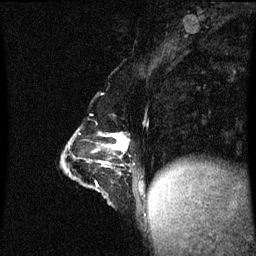
Breast MRI (dynamic contrast-enhanced), one sagittal slice. Position 22 of 60 along the scan axis. Dynamic contrast-enhanced series, image 2 of 3 at this slice position (ordered by acquisition). 1.5 T. TE 4.2 ms, TR 8.9 ms. 2 mm slice thickness. 256 × 256 image matrix, field of view 200 × 200 mm. Female patient, age 47 years. Case-level facts recorded for this patient, not image findings: setting: breast cancer imaged before/during neoadjuvant chemotherapy; receptor status: HR-positive, HER2-negative.
Structures marked on this image (semi-automatically segmented with operator editing):
- analysis volume of interest (the breast-tissue region the enhancement analysis was run in; not a lesion): bounding box (x1, y1, x2, y2) in pixels: (63, 122, 148, 205)
- tumour enhancement mask (voxels above the 70 % enhancement threshold inside the analysis volume of interest): (104, 134, 129, 151)